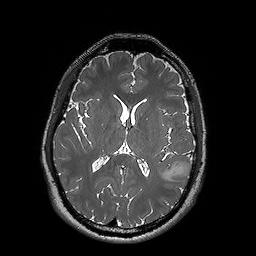
Brain MRI from a brain-tumour surgery series, one axial slice. Slice 81 of 192 in the series (ordered by position). 1 mm slice thickness. 256 × 256 image matrix. From the clinical record (not read from this slice): histopathology: Oligodendroglioma; WHO grade: 2; IDH mutation: yes; tumour location: Left Posterior Temporal.
Outlined on this slice (manually delineated by an expert):
- tumour: bounding box (x1, y1, x2, y2) in pixels: (159, 162, 193, 181)